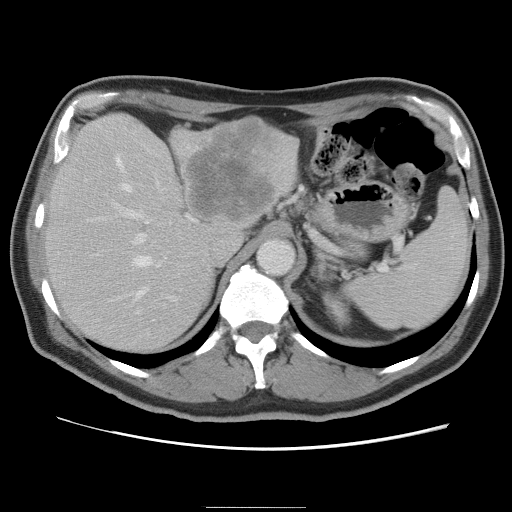
Contrast-enhanced abdominal CT, one axial slice. Position 56 of 87 along the scan axis. 120 kVp. Intravenous contrast given. Soft-tissue window (W 400 / L 40 HU). 5 mm slice thickness. 512 × 512 image matrix, field of view 363 × 363 mm. Male patient, age 63 years. From the clinical record (not read from this slice): diagnosis: colorectal cancer liver metastases, imaged before liver resection; multiple liver metastases: no; largest metastasis: 9 cm; chemotherapy before resection: no.
Outlined on this slice (expert manual segmentation):
- hepatic veins: bounding box (x1, y1, x2, y2) in pixels: (115, 157, 166, 322)
- liver: (44, 115, 299, 354)
- planned liver remnant (the part of the liver to remain after resection): (44, 151, 215, 354)
- portal vein (with intrahepatic branches): (96, 200, 197, 314)
- liver metastasis: (187, 122, 281, 221)